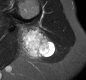
MRI of an extremity soft-tissue mass, one axial slice; position 14 of 30 along the scan axis; STIR; MR volume resampled by the dataset authors to the PET/CT grid (not the native acquisition matrix); 3.27 mm slice thickness; 86 × 80 image matrix, field of view 84 × 78 mm. Female patient. Case-level facts recorded for this patient, not image findings: histological type: malignant fibrous histiocytoma; grade: low; site of the primary tumour: left arm.
Structures marked on this image (expert contour drawn on MRI and transferred to this co-registered scan by the dataset authors):
- gross tumour volume (mass): bounding box <19,26,55,59> (left, top, right, bottom; pixels)